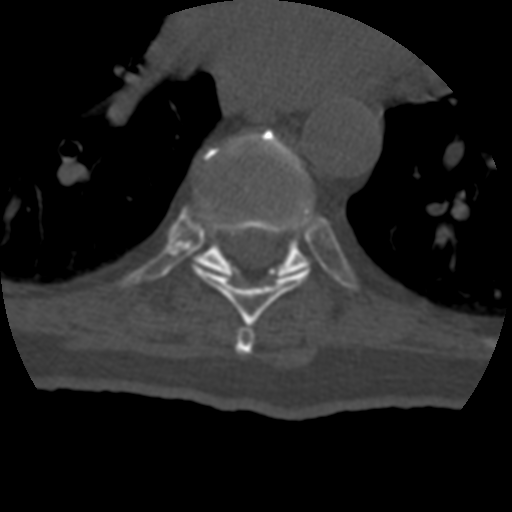
CT including the spine, one axial slice. Slice 252 of 399 in the series (ordered by position). Reconstruction kernel STANDARD. 120 kVp. Bone window (W 1800 / L 400 HU). 1.25 mm slice thickness. 512 × 512 image matrix, field of view 160 × 160 mm. Patient age 69 years. Case-level facts recorded for this patient, not image findings: primary cancer: prostate.
Structures marked on this image (semi-automatic segmentation, software-assisted and operator-edited):
- T7 vertebra: bounding box (x1, y1, x2, y2) in pixels: (235, 327, 255, 355)
- T8 vertebra: (193, 219, 310, 326)
- T9 vertebra: (197, 128, 310, 277)